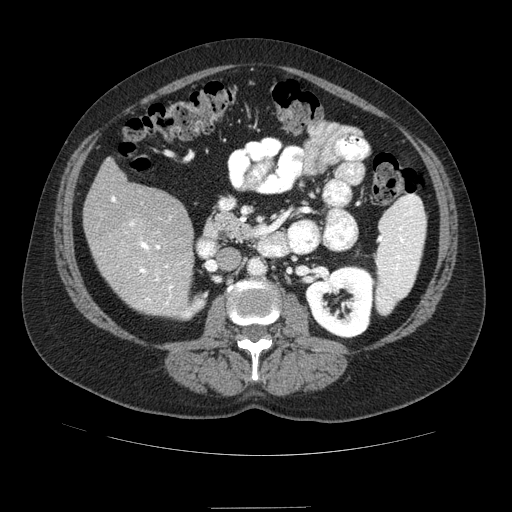
Contrast-enhanced abdominal CT (liver protocol), one axial slice. Position 30 of 89 along the scan axis. Soft-tissue window (W 400 / L 40 HU). 2.5 mm slice thickness. 512 × 512 image matrix, field of view 400 × 400 mm. From the clinical record (not read from this slice): diagnosis: hepatocellular carcinoma (patient treated with transarterial chemoembolisation; whether this scan precedes or follows treatment is not stated here); TNM stage (as recorded): Stage-IIIB; Child-Pugh class: A; tumour nodularity: multinodular.
Annotated regions visible in this slice (semi-automatic segmentation, software-assisted and operator-edited):
- liver parenchyma outside the tumour (the mass and vessels are separate outlines, so this box may not span the whole liver): bounding box [x1, y1, x2, y2] px = [84, 158, 194, 314]
- liver vessels: [111, 196, 173, 305]